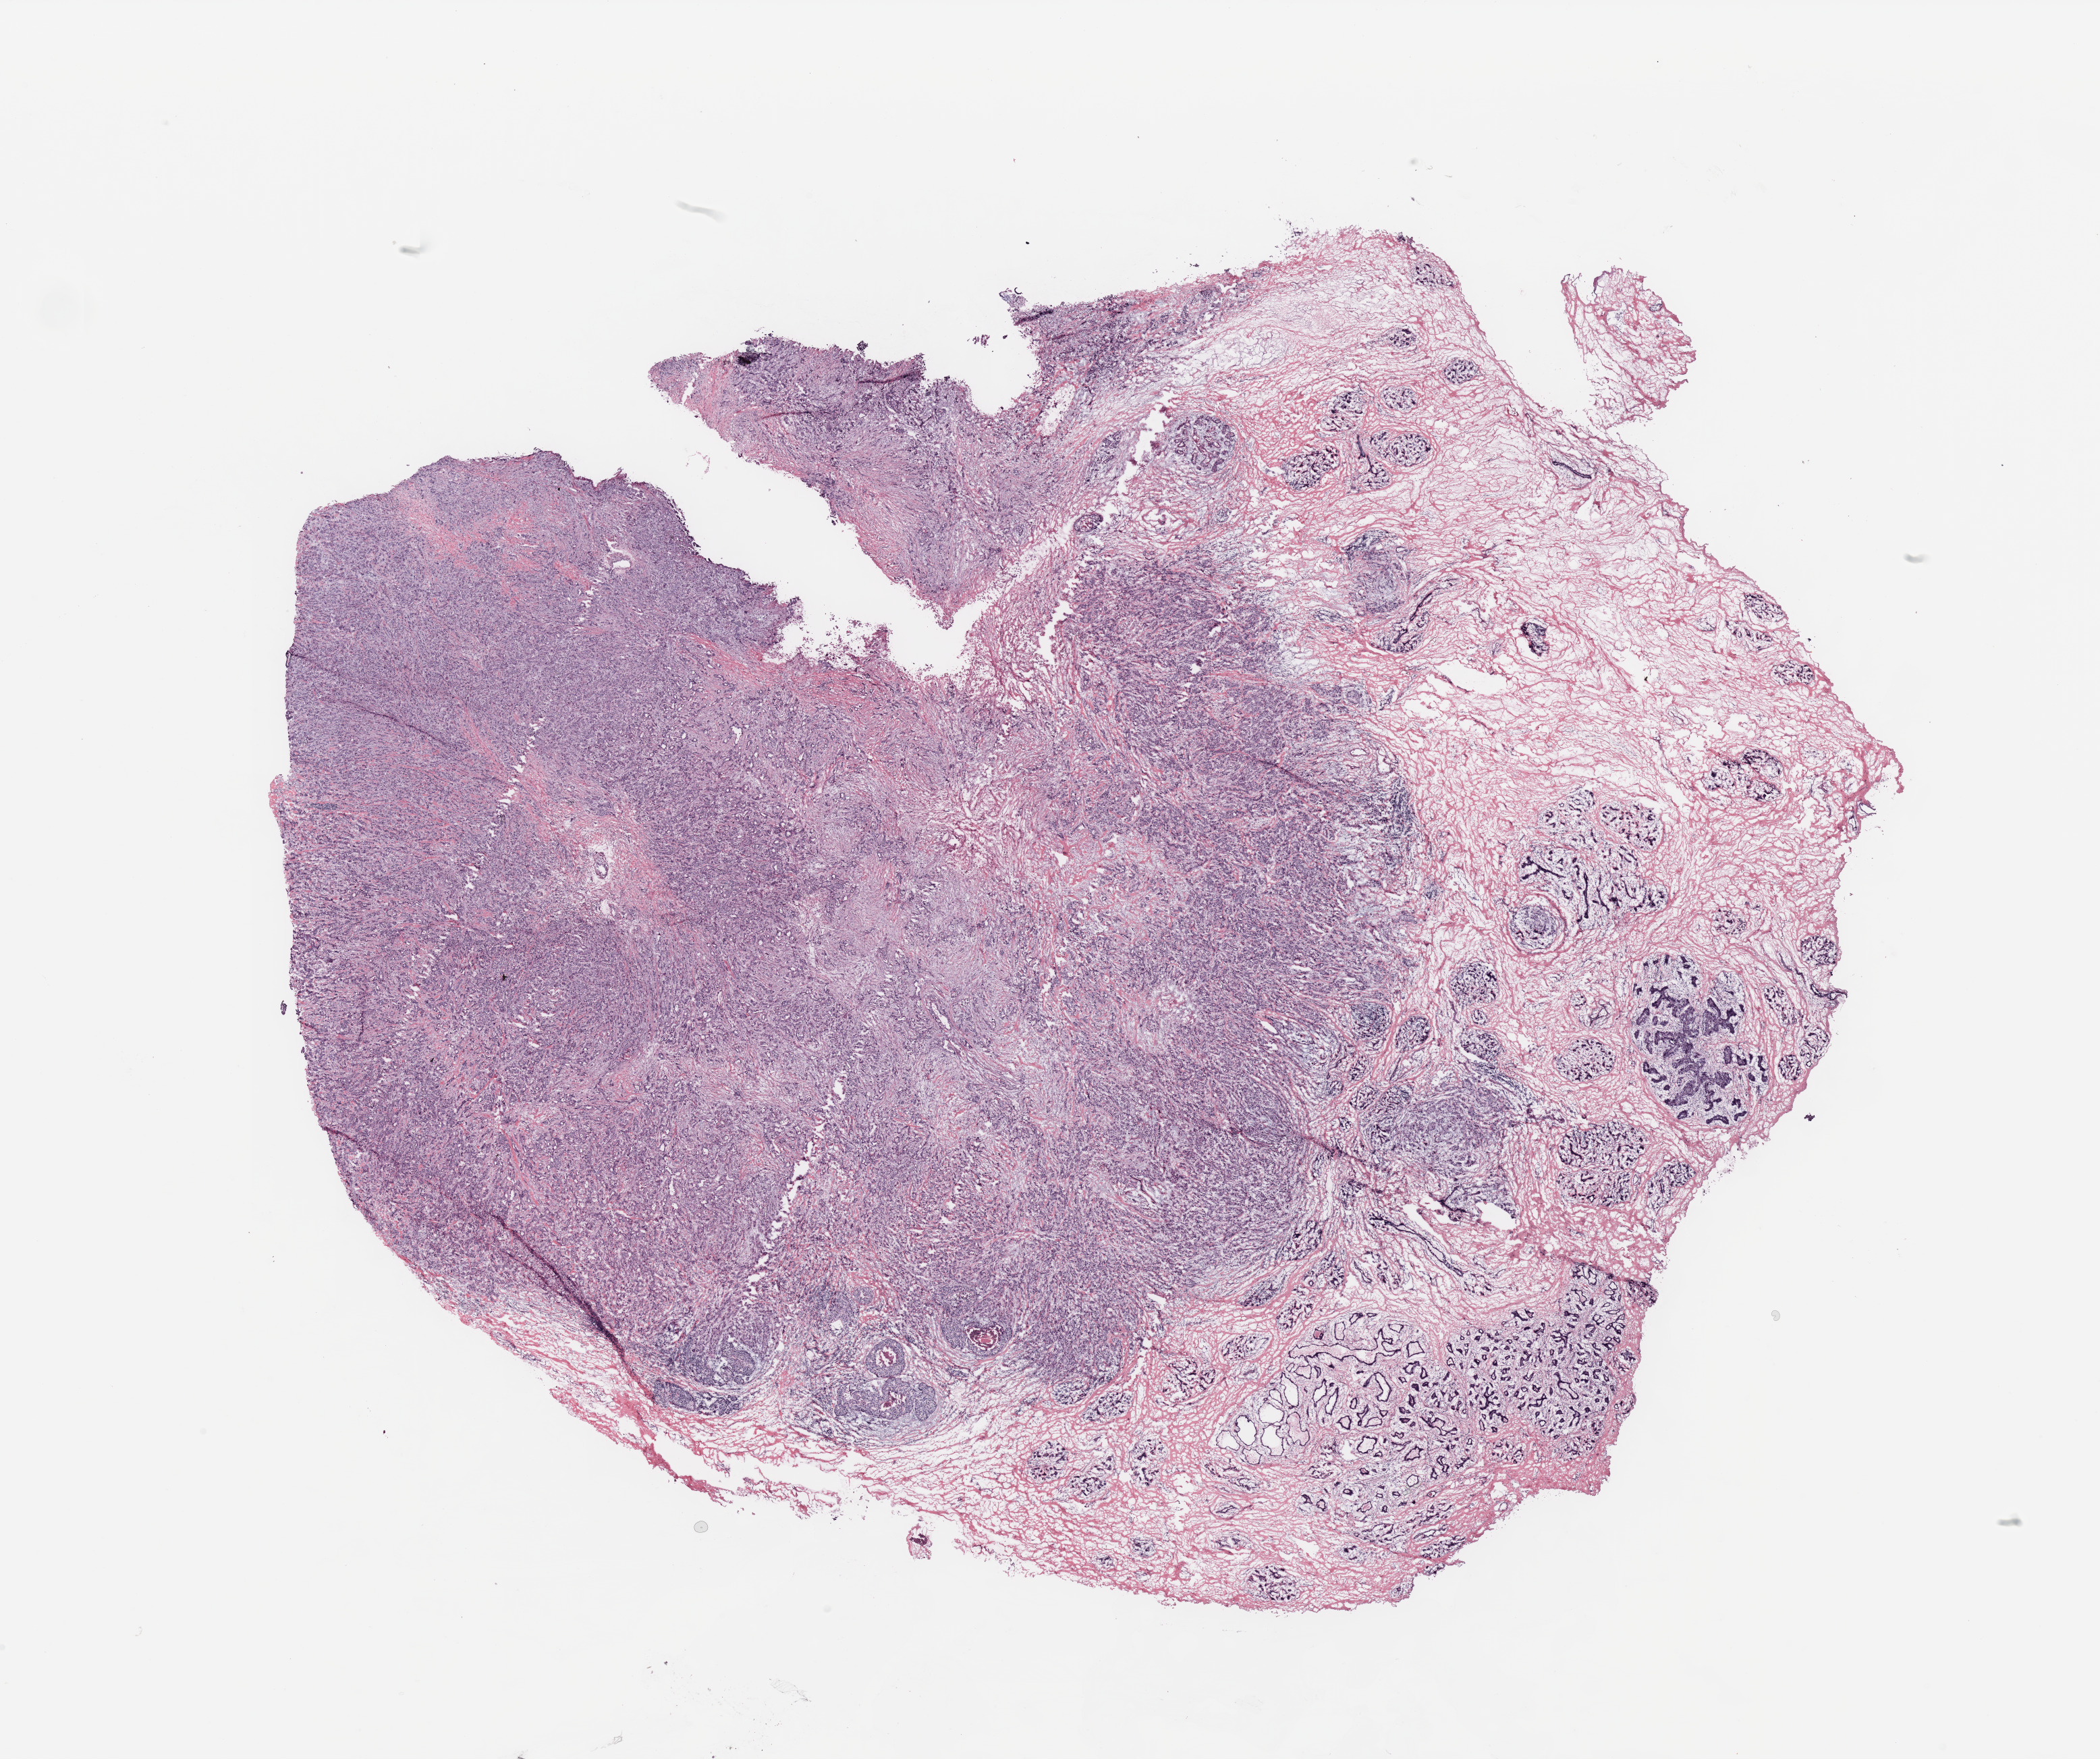
H&E-stained whole-slide image, shown as a low-resolution overview of the whole scanned area (about 24.6 x 20.6 mm); tumour tissue sample, breast. Female, 35 y/o.
AJCC pathologic stage: IIB. Diagnosis: Infiltrating duct carcinoma, NOS.